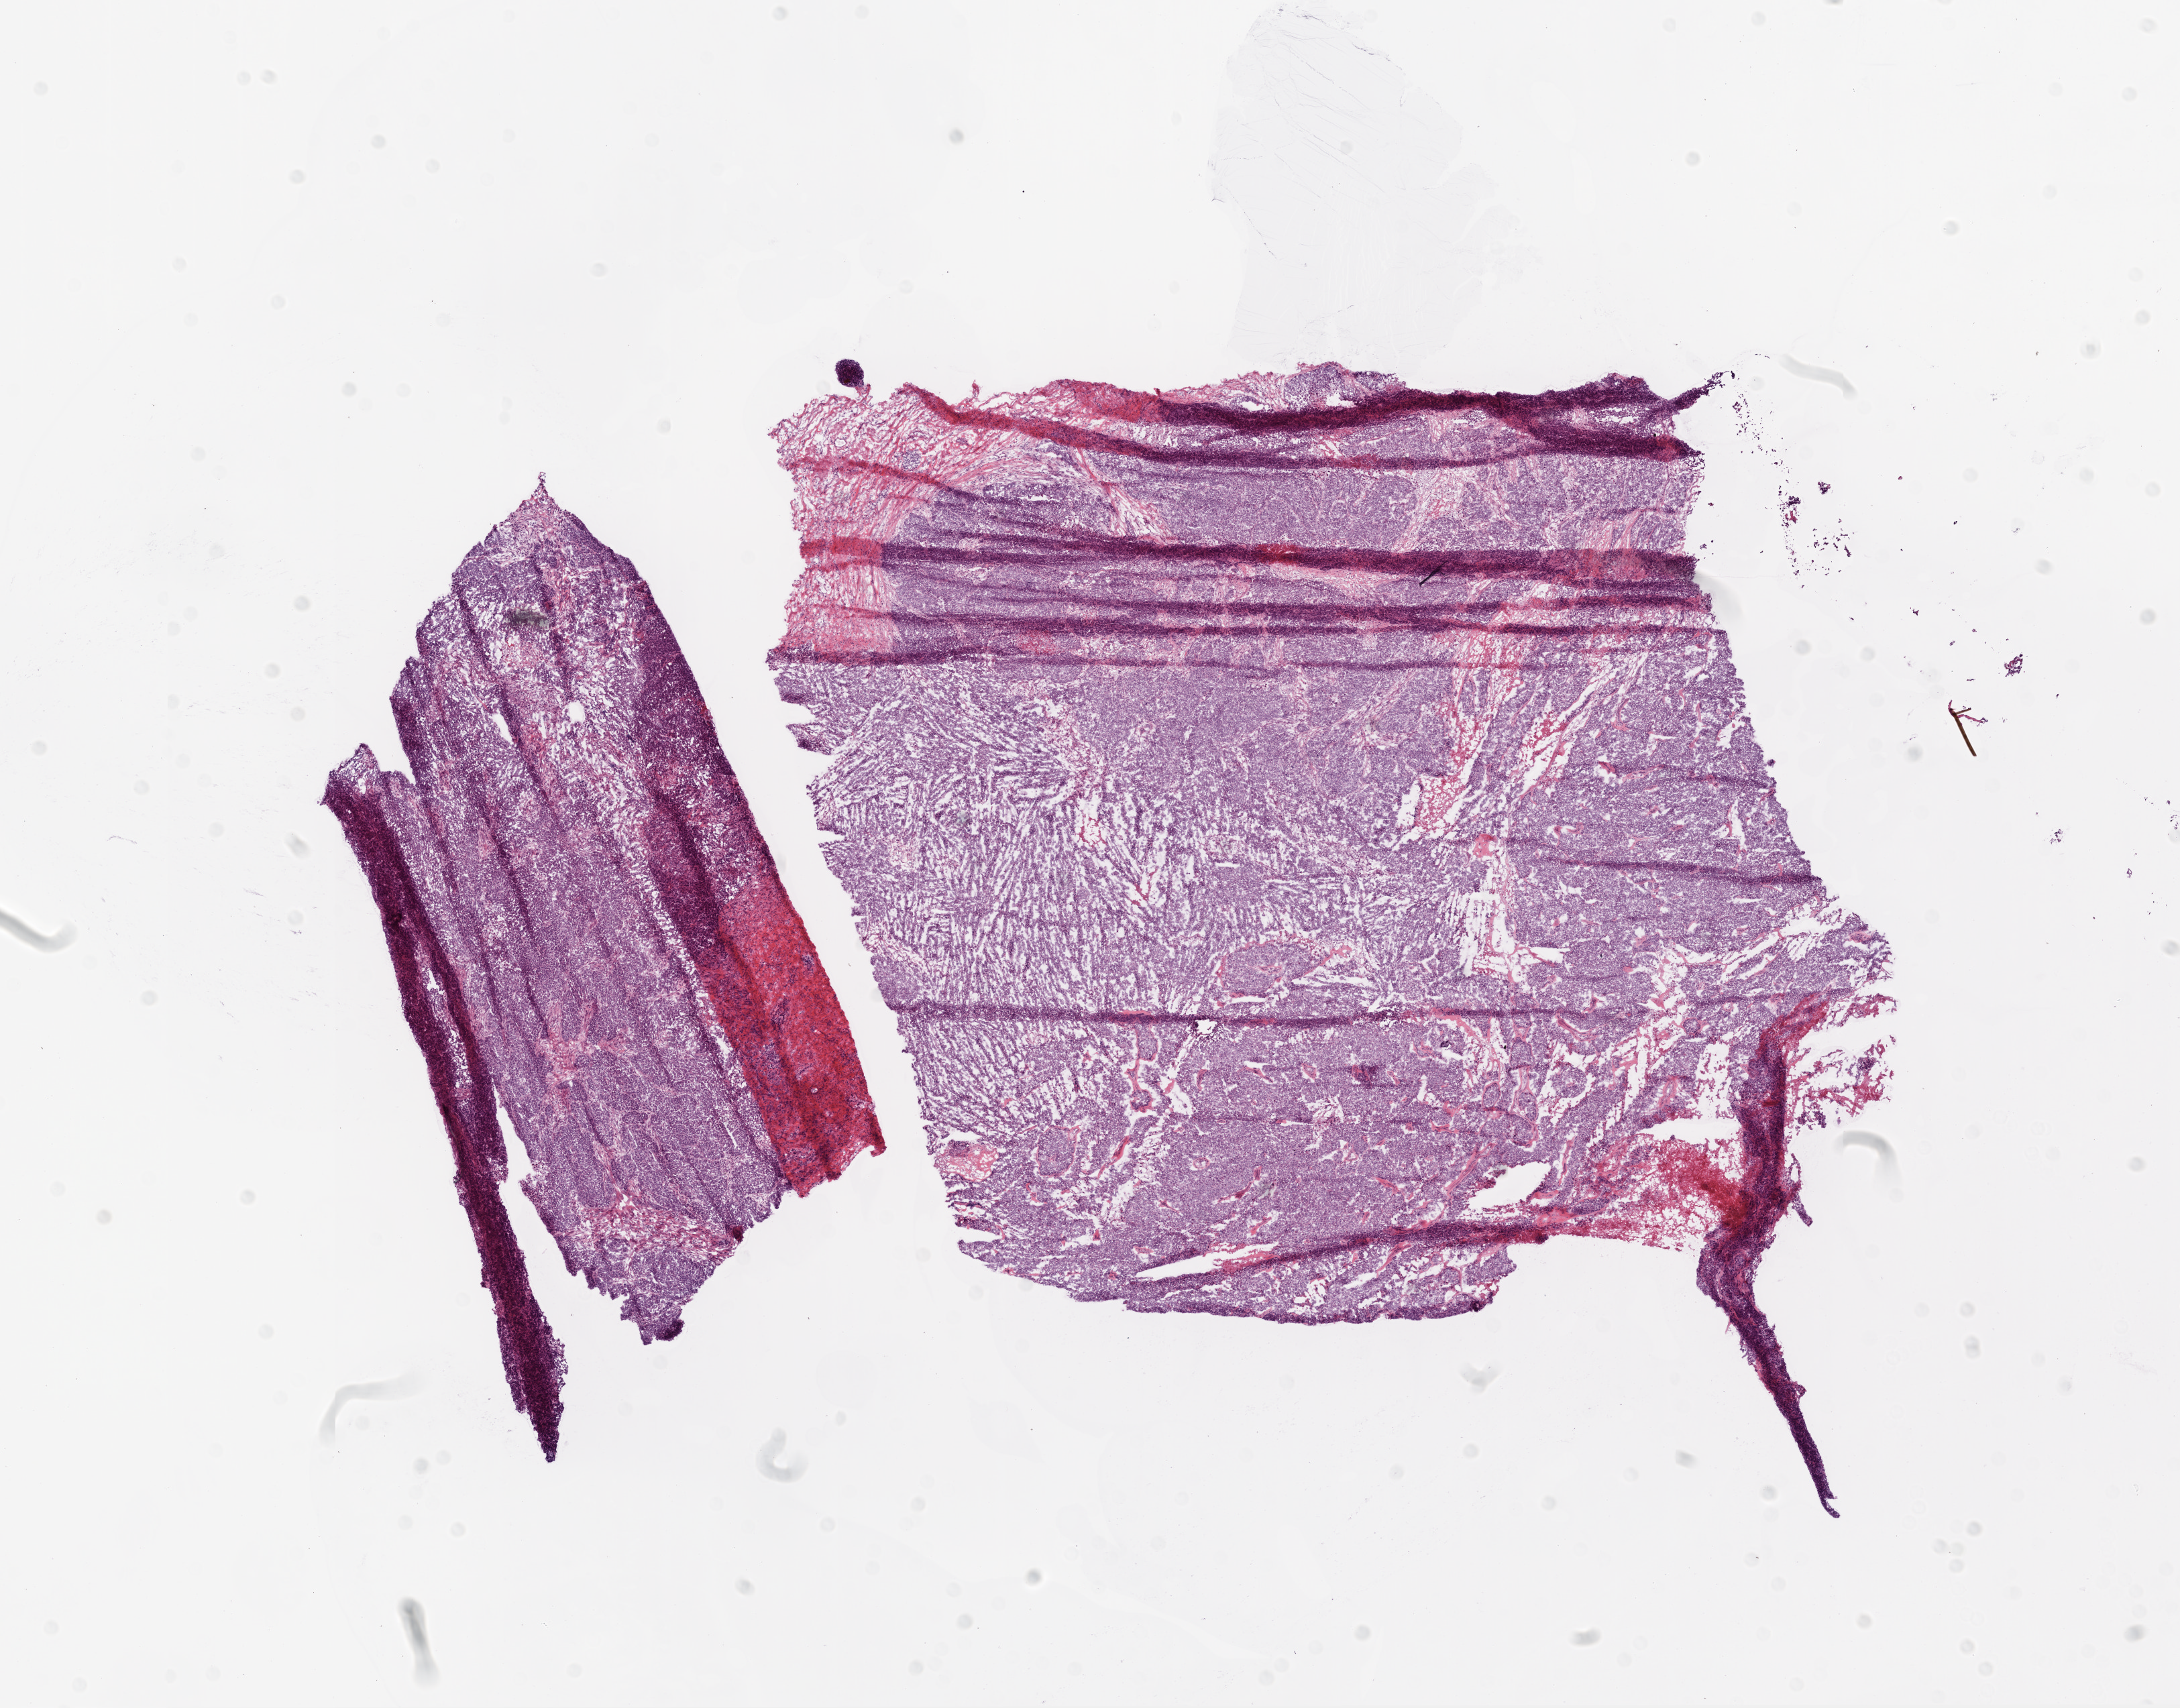
Whole-slide histology image, Hematoxylin and eosin (H&E) stained, shown as a low-resolution overview of the whole scanned area (about 13.0 x 10.2 mm); frozen section from the bottom of the tissue portion; ovary, primary tumour sample. Female patient; age at initial diagnosis 67 years. Histologic grade: G3 (poorly differentiated). Pathologist review of this section (percent, as recorded): tumour cells 79%, tumour nuclei 90%, normal cells 8%, stromal cells 5%, necrosis 8%.
FIGO stage: IIIC. Diagnosis: Serous cystadenocarcinoma, NOS. Laterality: bilateral.